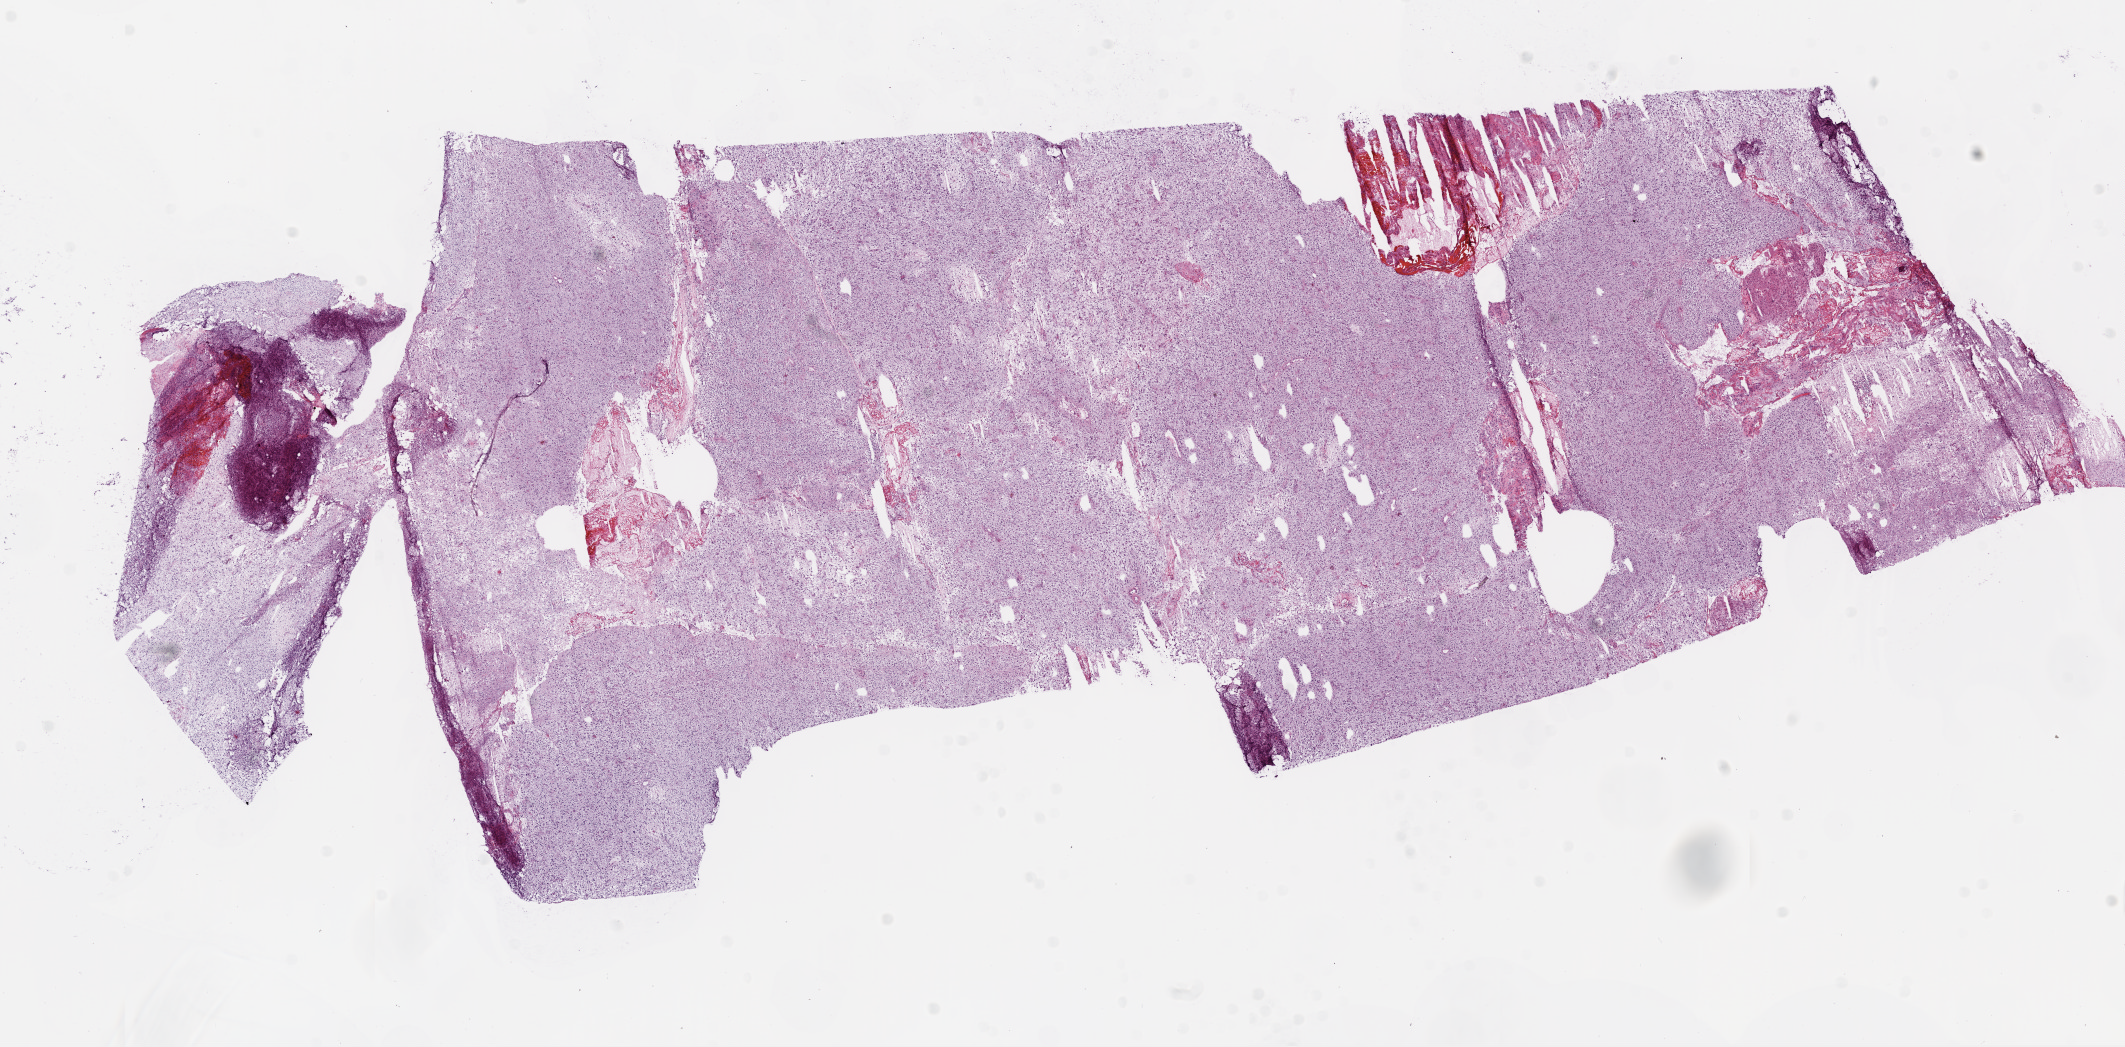
Digitized H&E-stained tissue section (whole slide) — a low-resolution overview of the entire scanned area, about 17.1 x 8.4 mm (from a 20x scan). Frozen section from the bottom of the tissue portion. Primary tumour sample from the brain. Male patient; age at initial diagnosis 88 years. Pathologist review of this section (percent, as recorded): tumour cells 90%, tumour nuclei 85%, normal cells 0%, stromal cells 0%, necrosis 10%.
* diagnosis: Glioblastoma